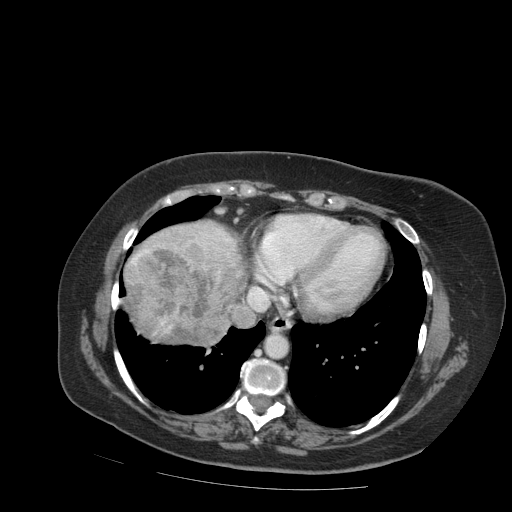
Contrast-enhanced abdominal CT (liver protocol), one axial slice. Position 83 of 99 along the scan axis. Soft-tissue window (W 400 / L 40 HU). 2.5 mm slice thickness. 512 × 512 image matrix, field of view 400 × 400 mm. Case-level facts recorded for this patient, not image findings: diagnosis: hepatocellular carcinoma (patient treated with transarterial chemoembolisation; whether this scan precedes or follows treatment is not stated here); TNM stage (as recorded): Stage-IVB; Child-Pugh class: A; tumour differentiation: moderately differentiated; tumour nodularity: uninodular.
Structures marked on this image (semi-automatically segmented with operator editing):
- liver parenchyma outside the tumour (the mass and vessels are separate outlines, so this box may not span the whole liver): bounding box <124,220,243,346> (left, top, right, bottom; pixels)
- mass: <125,244,244,346>
- liver vessels: <203,232,231,244>